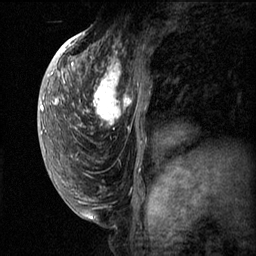
Breast MRI (dynamic contrast-enhanced), one sagittal slice. Slice 32 of 60 in the series (ordered by position). Dynamic contrast-enhanced series, image 2 of 3 at this slice position (ordered by acquisition). 1.5 T. TE 4.2 ms, TR 11.1 ms. 2 mm slice thickness. 256 × 256 image matrix, field of view 180 × 180 mm. Female patient, age 50 years.
Outlined on this slice (semi-automatic segmentation, software-assisted and operator-edited):
- analysis volume of interest (the breast-tissue region the enhancement analysis was run in; not a lesion): box from (x=82, y=56) to (x=150, y=143) px
- tumour enhancement mask (voxels above the 70 % enhancement threshold inside the analysis volume of interest): (x=83, y=60)–(x=138, y=125)